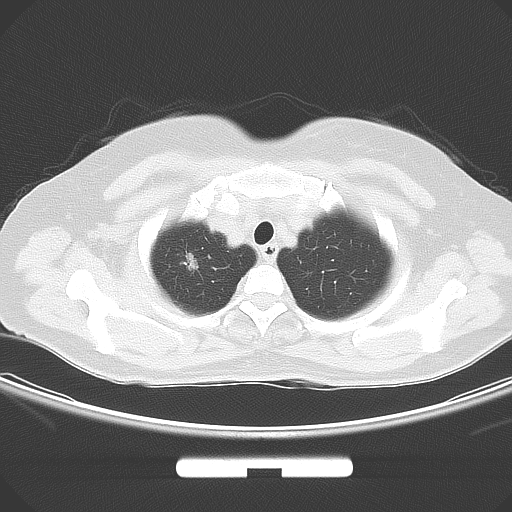
Chest CT, one axial slice. 120 kVp. Lung window (W 1500 / L -600 HU). 512 × 512 image matrix, field of view 369 × 369 mm. Patient: female, 58 years. Case-level facts recorded for this patient, not image findings: clinical TNM (as recorded): T1b N0 M0; histopathological grade: G2-3.
Annotated regions visible in this slice (bounding box drawn by a radiologist):
- lung tumour (recorded histology: adenocarcinoma): box from (x=173, y=243) to (x=207, y=278) px